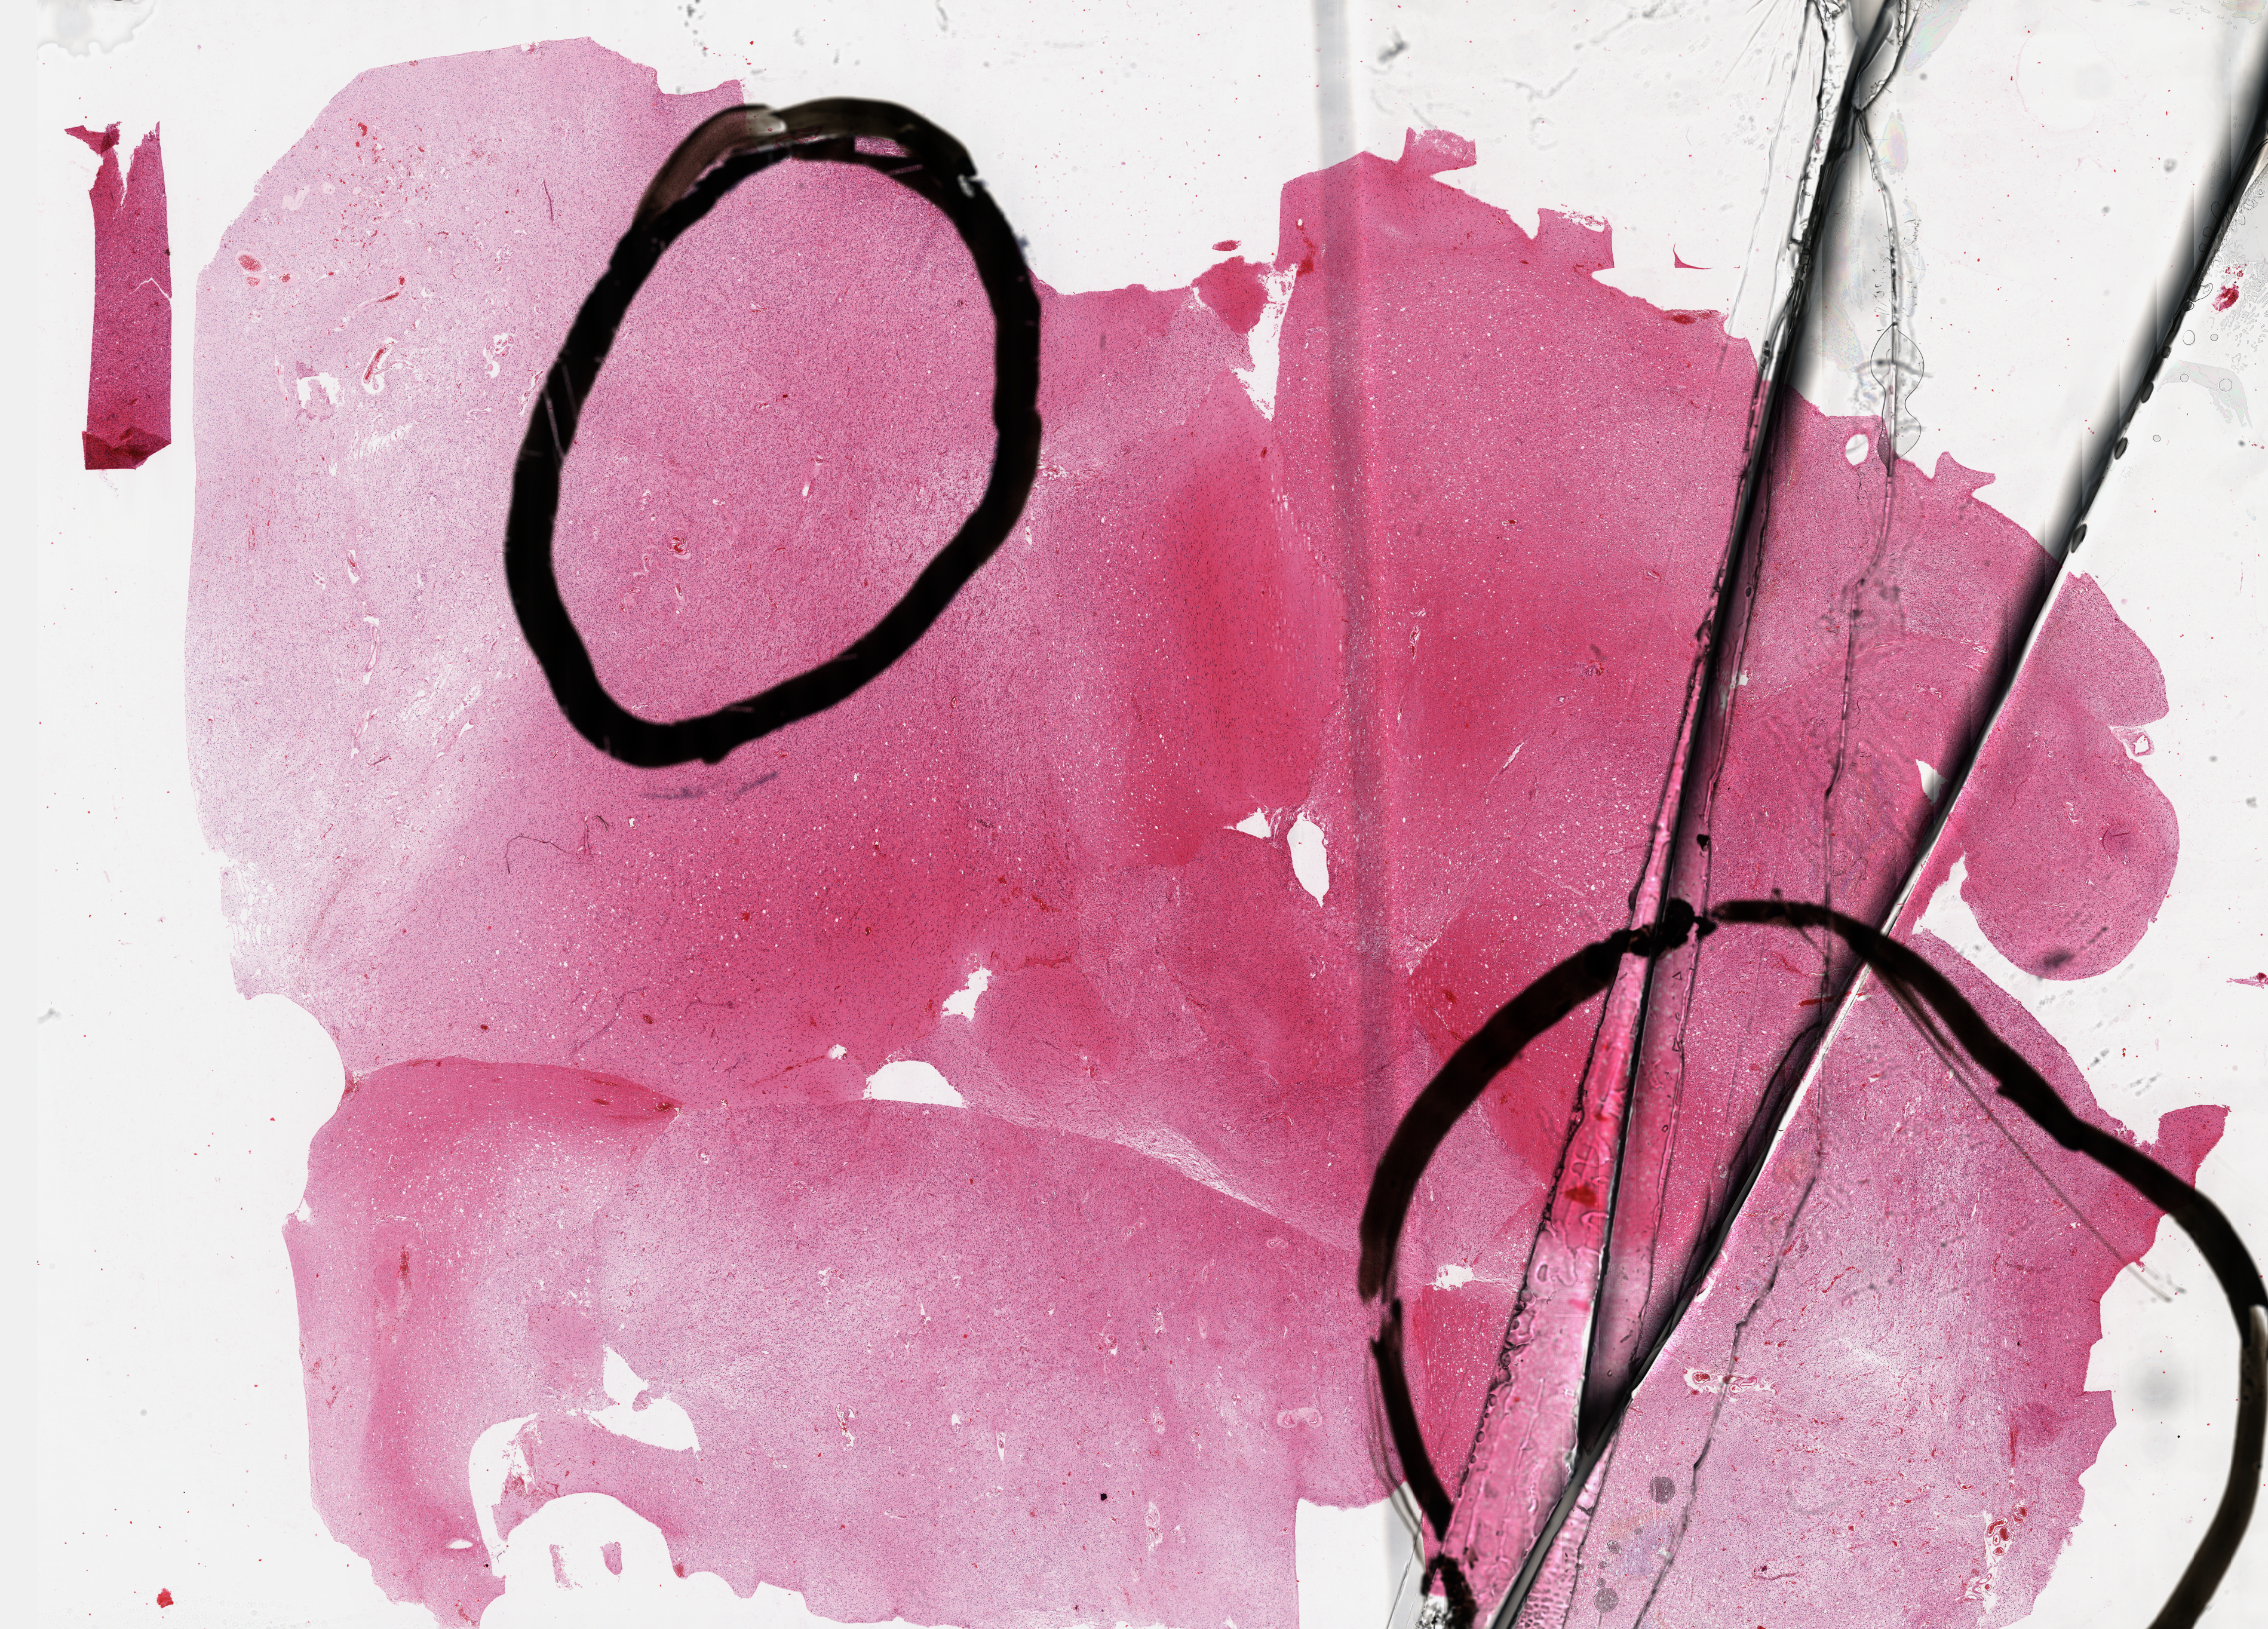
Digitized Hematoxylin and eosin (H&E) stained tissue section (whole slide), whole scanned area (about 30.7 x 22.0 mm) shown as a low-resolution overview, FFPE section, sample: primary tumour, brain. Patient: male, age at initial diagnosis 46 years. Histologic grade: G3 (poorly differentiated).
• diagnosis: Astrocytoma, anaplastic
• laterality: left